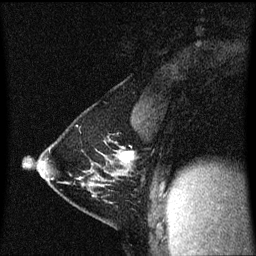
Breast MRI (dynamic contrast-enhanced), one sagittal slice. Position 35 of 60 along the scan axis. Dynamic contrast-enhanced series, image 2 of 3 at this slice position (ordered by acquisition). 1.5 T. TE 4.2 ms, TR 8.4 ms. 256 × 256 image matrix. Female patient, age 40 years. From the clinical record (not read from this slice): setting: breast cancer imaged before/during neoadjuvant chemotherapy; receptor status: triple-negative.
Annotated regions visible in this slice (semi-automatically segmented with operator editing):
- analysis volume of interest (the breast-tissue region the enhancement analysis was run in; not a lesion): bounding box [x1, y1, x2, y2] px = [37, 142, 135, 197]
- tumour enhancement mask (voxels above the 70 % enhancement threshold inside the analysis volume of interest): [120, 152, 132, 163]